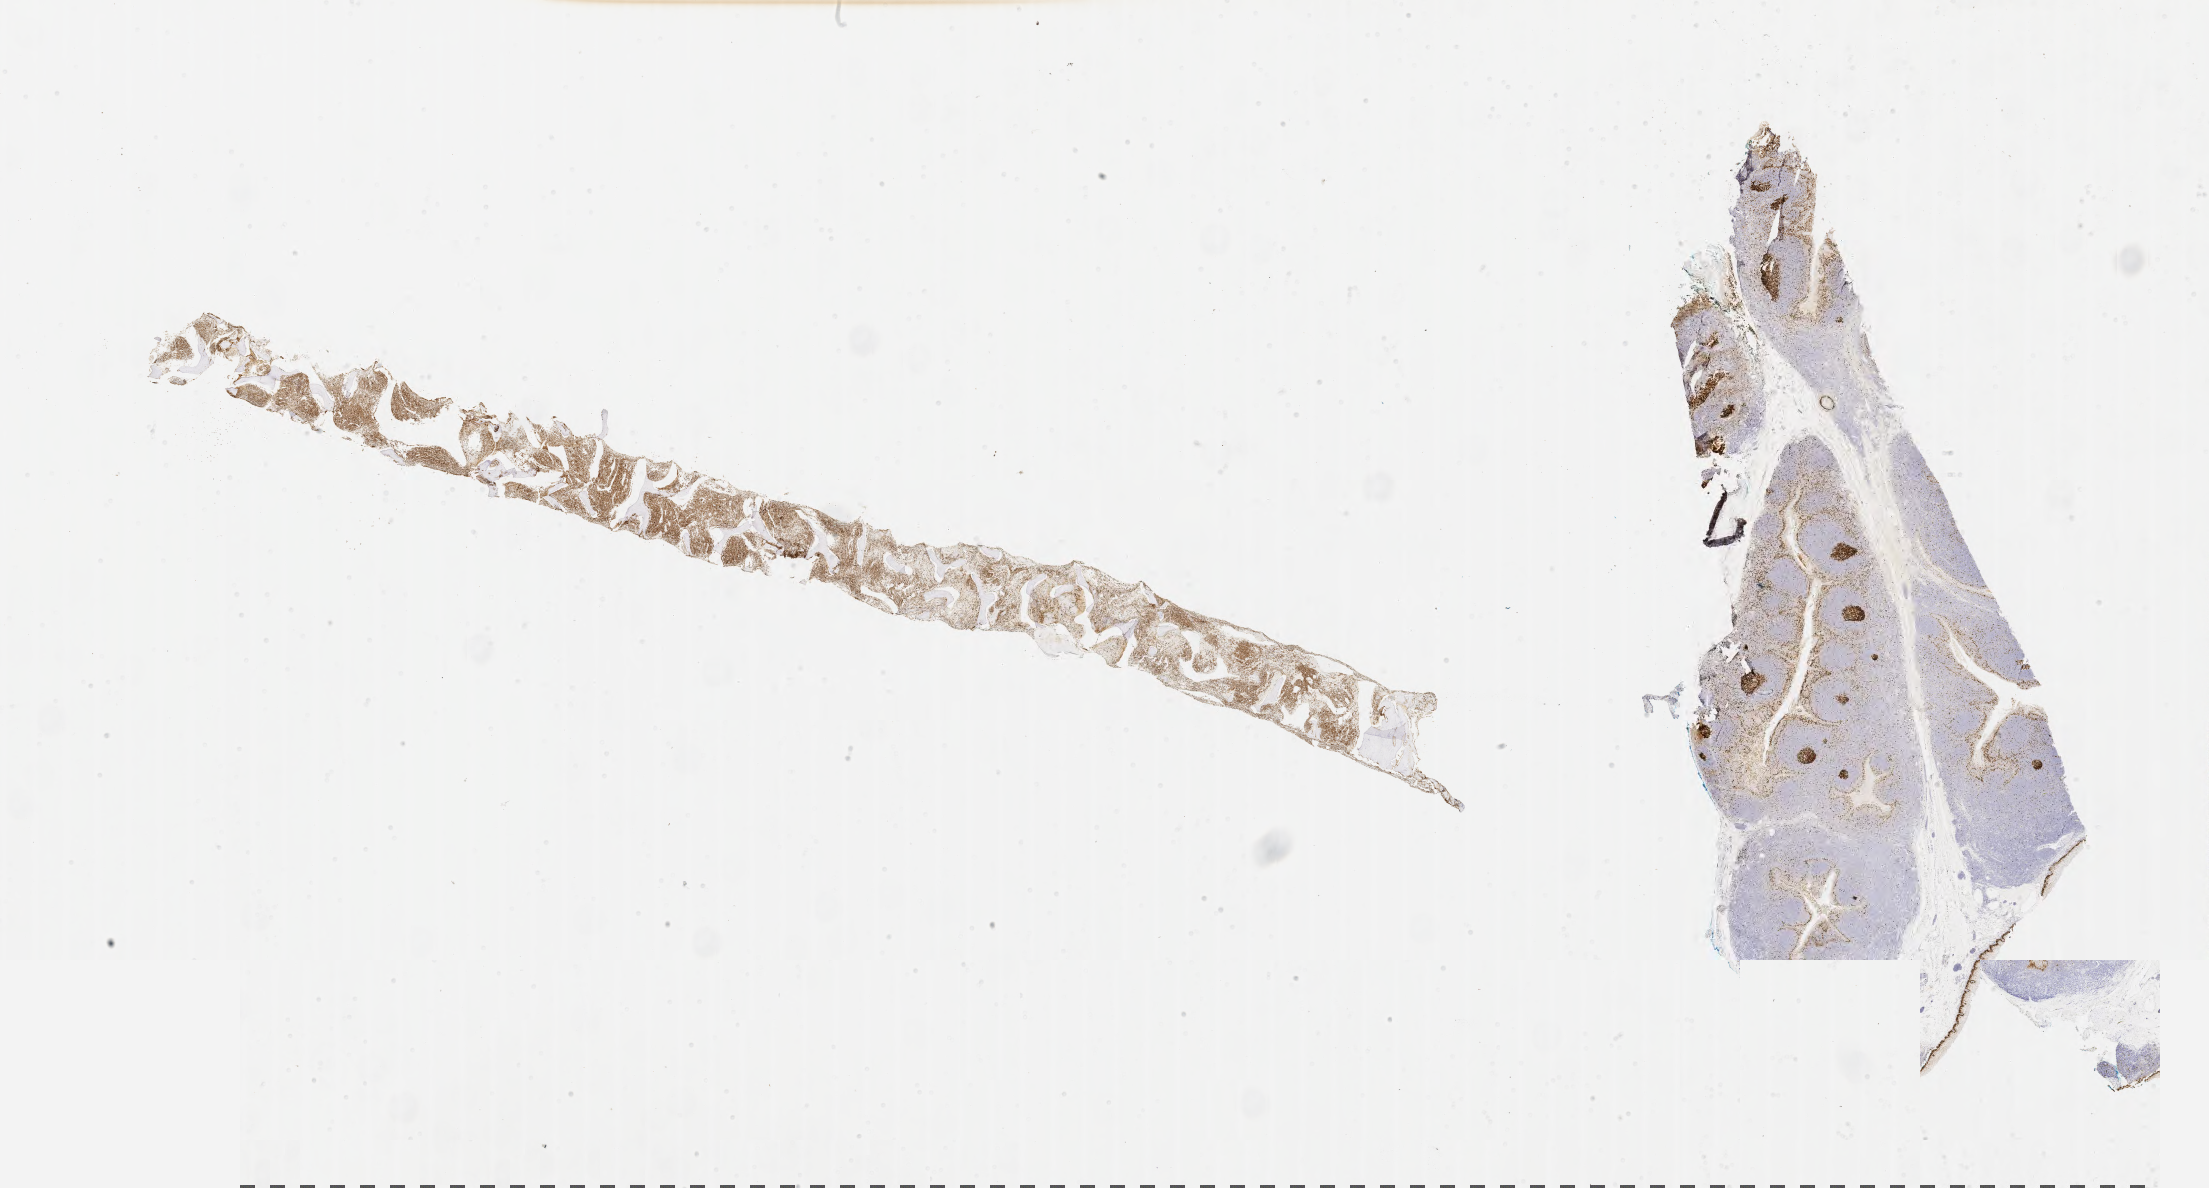
Whole-slide image, immunohistochemical stain for Ki-67 — whole scanned area (about 35.7 x 19.2 mm) shown as a low-resolution overview. Specimen: tumor tissue. Anatomic site: bone marrow. Patient male; age 18 years.
- diagnosis: Burkitt lymphoma, NOS